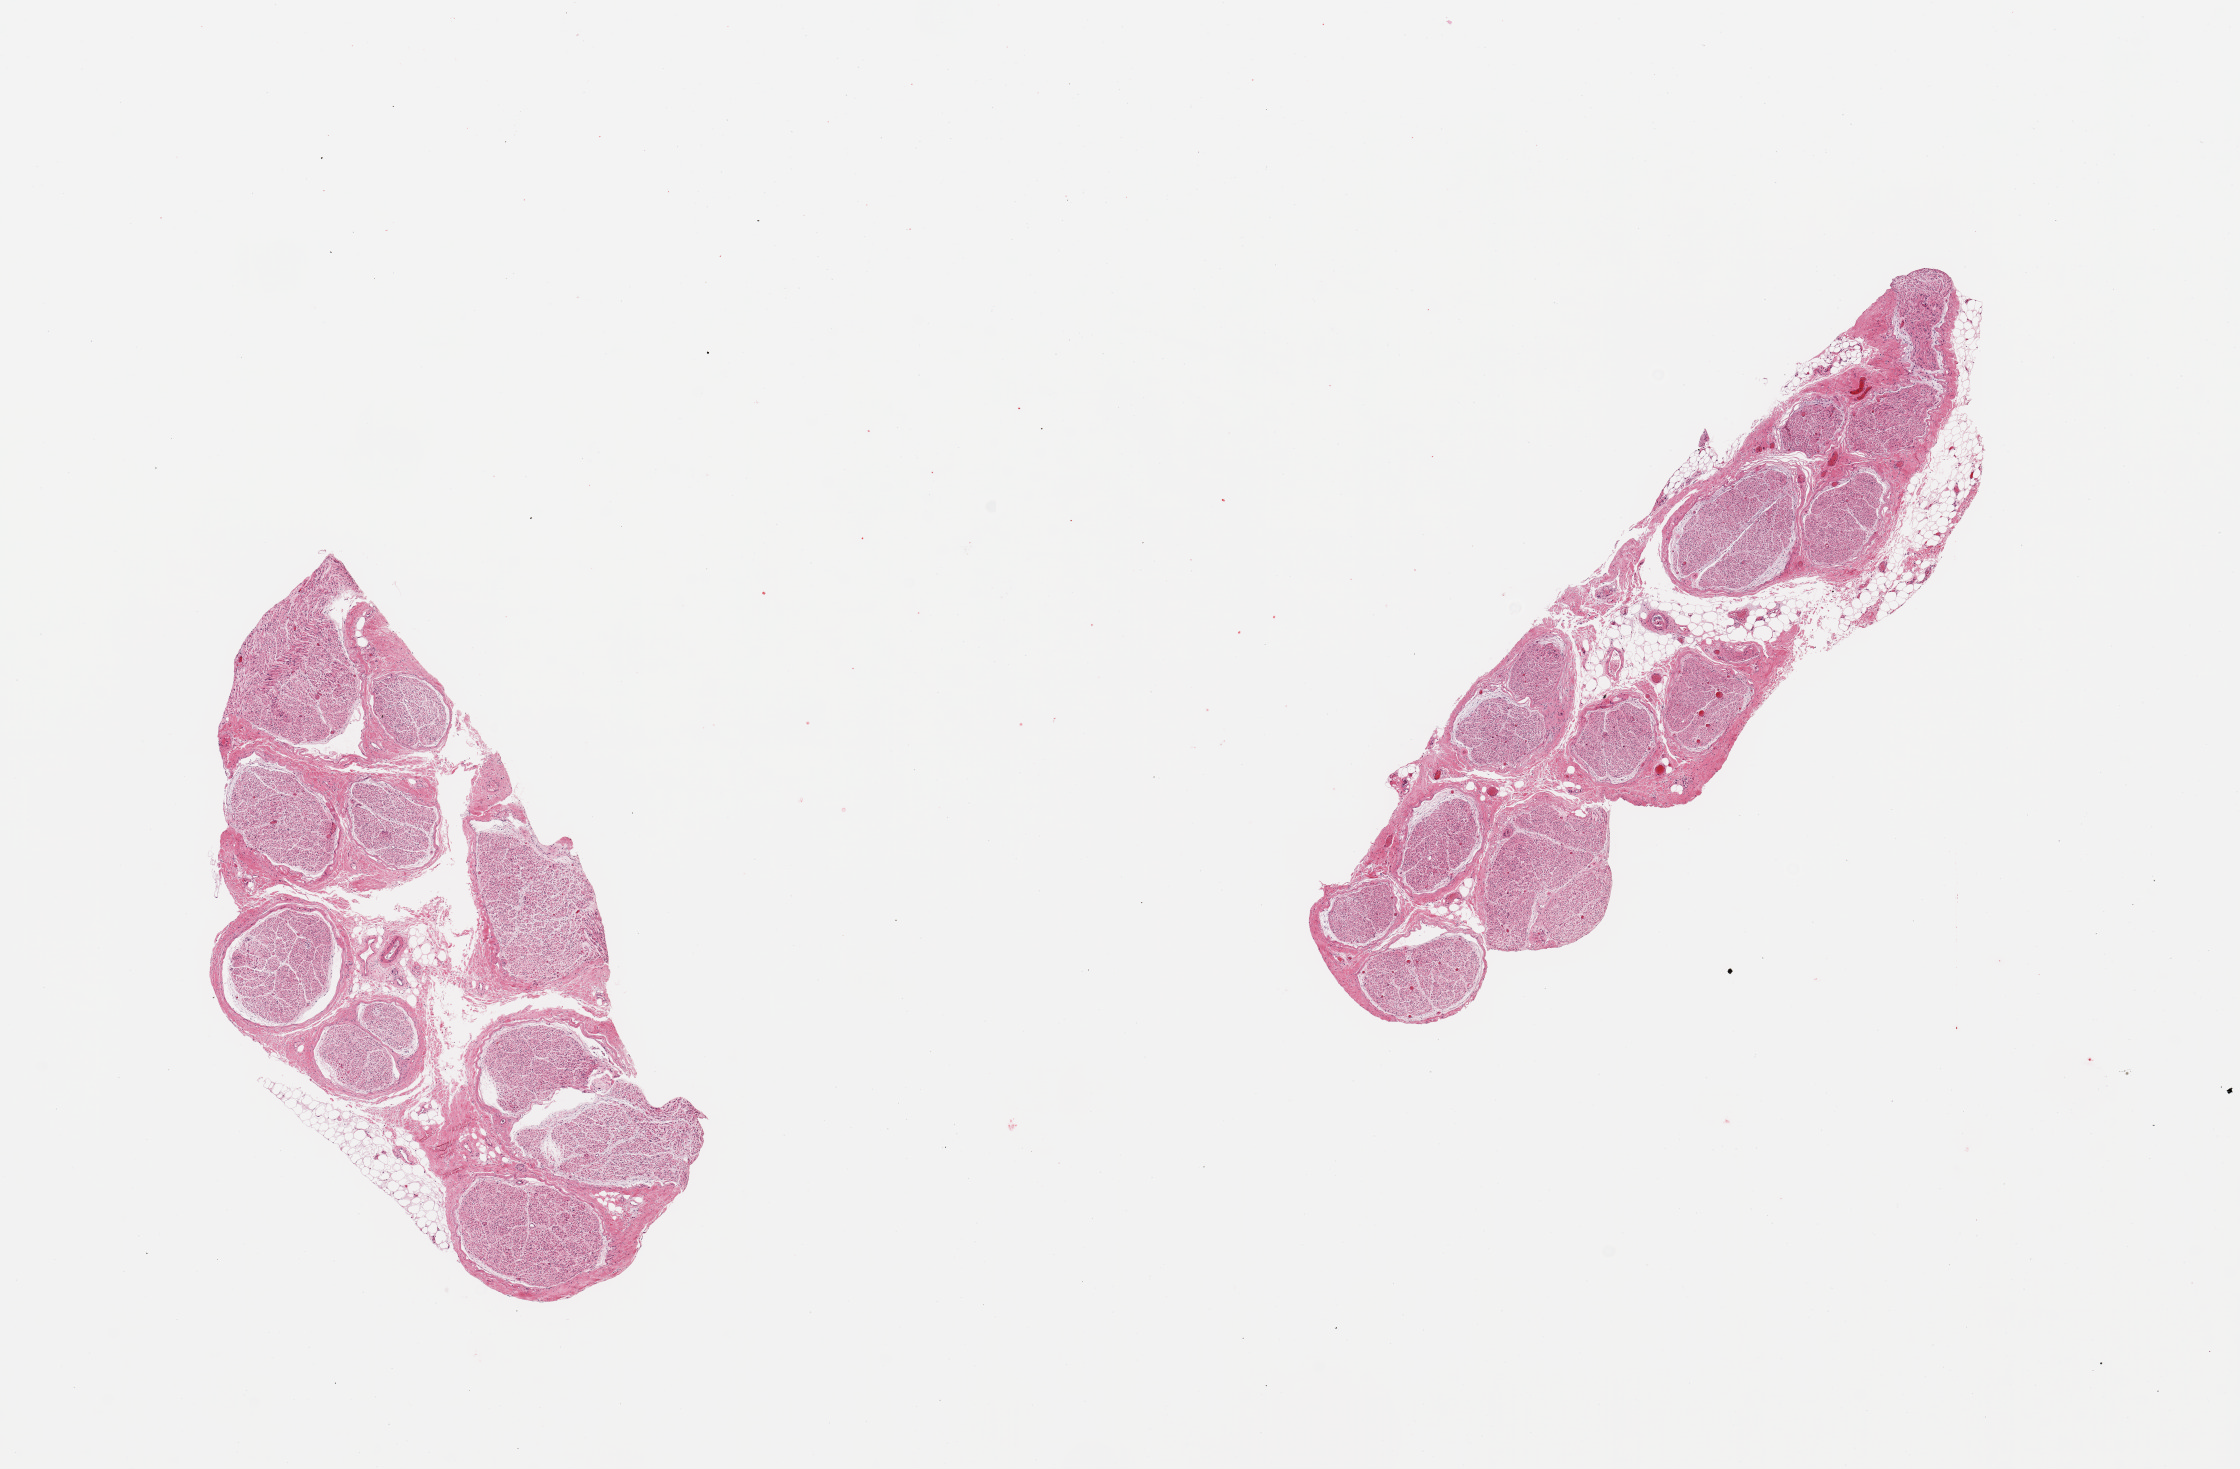
Whole-slide image, H&E stain, brightfield — whole scanned area (about 17.7 x 11.6 mm, from a 20x scan) shown as a low-resolution overview, PAXgene-fixed, paraffin-embedded tissue, sampled site (target tissue): tibial nerve, tissue donor sample. Female donor.
Reviewer comment on this tissue sample: 2 pieces, trace adherent fat, good specimens.